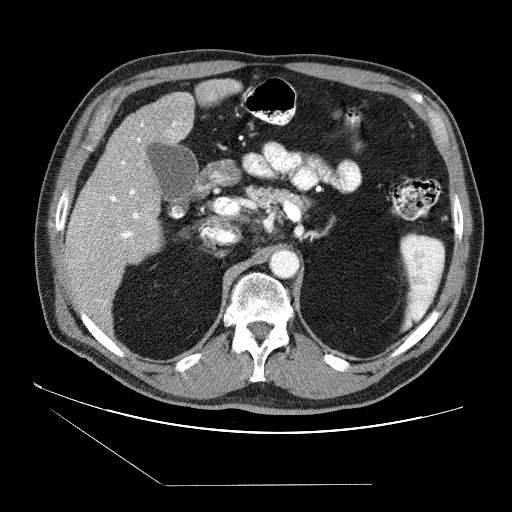
Contrast-enhanced abdominal CT (liver protocol), one axial slice; reconstruction kernel STANDARD; 120 kVp; soft-tissue window (W 400 / L 40 HU); 2.5 mm slice thickness; 512 × 512 image matrix, field of view 400 × 400 mm. From the clinical record (not read from this slice): diagnosis: hepatocellular carcinoma (patient treated with transarterial chemoembolisation; whether this scan precedes or follows treatment is not stated here); TNM stage (as recorded): Stage-II; Child-Pugh class: B; tumour nodularity: multinodular; tumour size: 2.6 cm.
Structures marked on this image (semi-automatically segmented with operator editing):
- liver parenchyma outside the tumour (the mass and vessels are separate outlines, so this box may not span the whole liver): bounding box (x1, y1, x2, y2) in pixels: (64, 78, 240, 325)
- liver vessels: (71, 85, 237, 318)